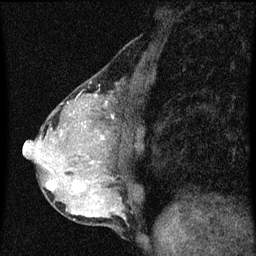
Breast MRI (dynamic contrast-enhanced), one sagittal slice. Position 22 of 60 along the scan axis. Dynamic contrast-enhanced series, image 2 of 3 at this slice position (ordered by acquisition). 1.5 T. TE 4.2 ms, TR 8 ms. 2 mm slice thickness. 256 × 256 image matrix, field of view 180 × 180 mm. Patient: female, 49 years.
Outlined on this slice (semi-automatic segmentation, software-assisted and operator-edited):
- analysis volume of interest (the breast-tissue region the enhancement analysis was run in; not a lesion): bounding box (x1, y1, x2, y2) in pixels: (44, 174, 89, 201)
- tumour enhancement mask (voxels above the 70 % enhancement threshold inside the analysis volume of interest): (46, 180, 84, 193)